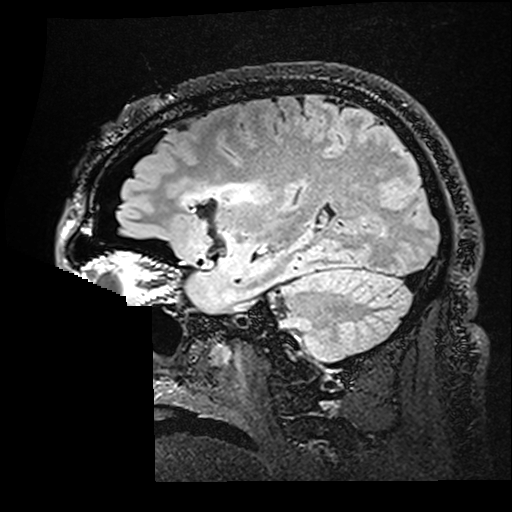
Brain MRI from a brain-tumour surgery series, one sagittal slice; slice 117 of 176 in the series (ordered by position); T2 FLAIR; 1 mm slice thickness; 512 × 512 image matrix, field of view 250 × 250 mm. Case-level facts recorded for this patient, not image findings: histopathology: Astrocytoma; WHO grade: 2; IDH mutation: yes; tumour location: Right Insular.
Annotated regions visible in this slice (expert manual segmentation):
- residual tumour: bounding box (x1, y1, x2, y2) in pixels: (181, 182, 248, 207)